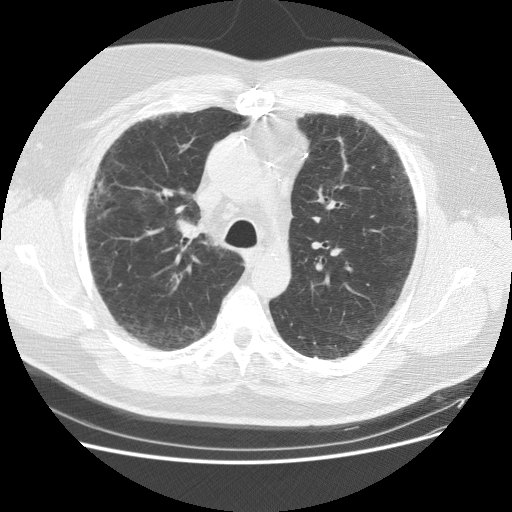
Chest CT (low-dose screening protocol), one axial image. Baseline screening round. Lung window (W 1500 / L -600 HU). 2.5 mm slice thickness. Slice 42 of 151 in the series. Male participant, aged 59 years at enrolment. Current smoker at enrolment.
Lesion marked by an expert reader, bounding box (x1, y1, x2, y2) in pixels: (82, 158, 126, 244). The screening reader recorded 2 non-calcified nodules or masses ≥4 mm on this exam (right middle lobe, right lower lobe); which of them this box marks is not recorded. Official screen result: positive, change unspecified: nodule(s) >= 4 mm or enlarging nodule(s), mass(es), or other non-specific abnormalities suspicious for lung cancer. Lung cancer was diagnosed 338 days after this screen: adenocarcinoma, NOS, right upper lobe, right middle lobe, moderately differentiated (G2), stage IA (AJCC 6th edition), 13 mm at pathology.